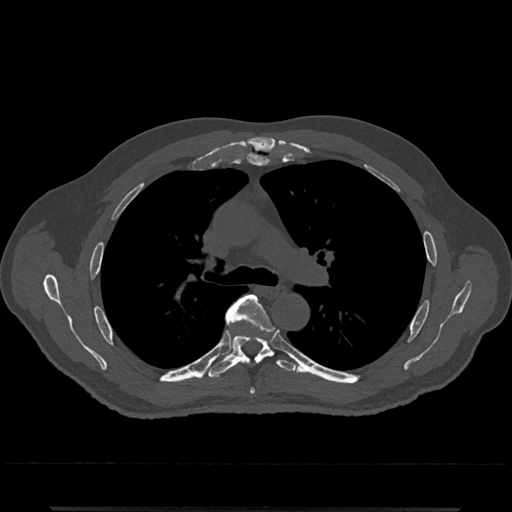
CT including the spine, one axial slice; bone window (W 1800 / L 400 HU); 512 × 512 image matrix, field of view 393 × 393 mm. Patient: male, 67 years. Case-level facts recorded for this patient, not image findings: primary cancer: prostate.
Outlined on this slice (semi-automatic segmentation, software-assisted and operator-edited):
- T5 vertebra: box from (x=225, y=294) to (x=270, y=328) px
- T6 vertebra: (x=207, y=305)–(x=297, y=379)